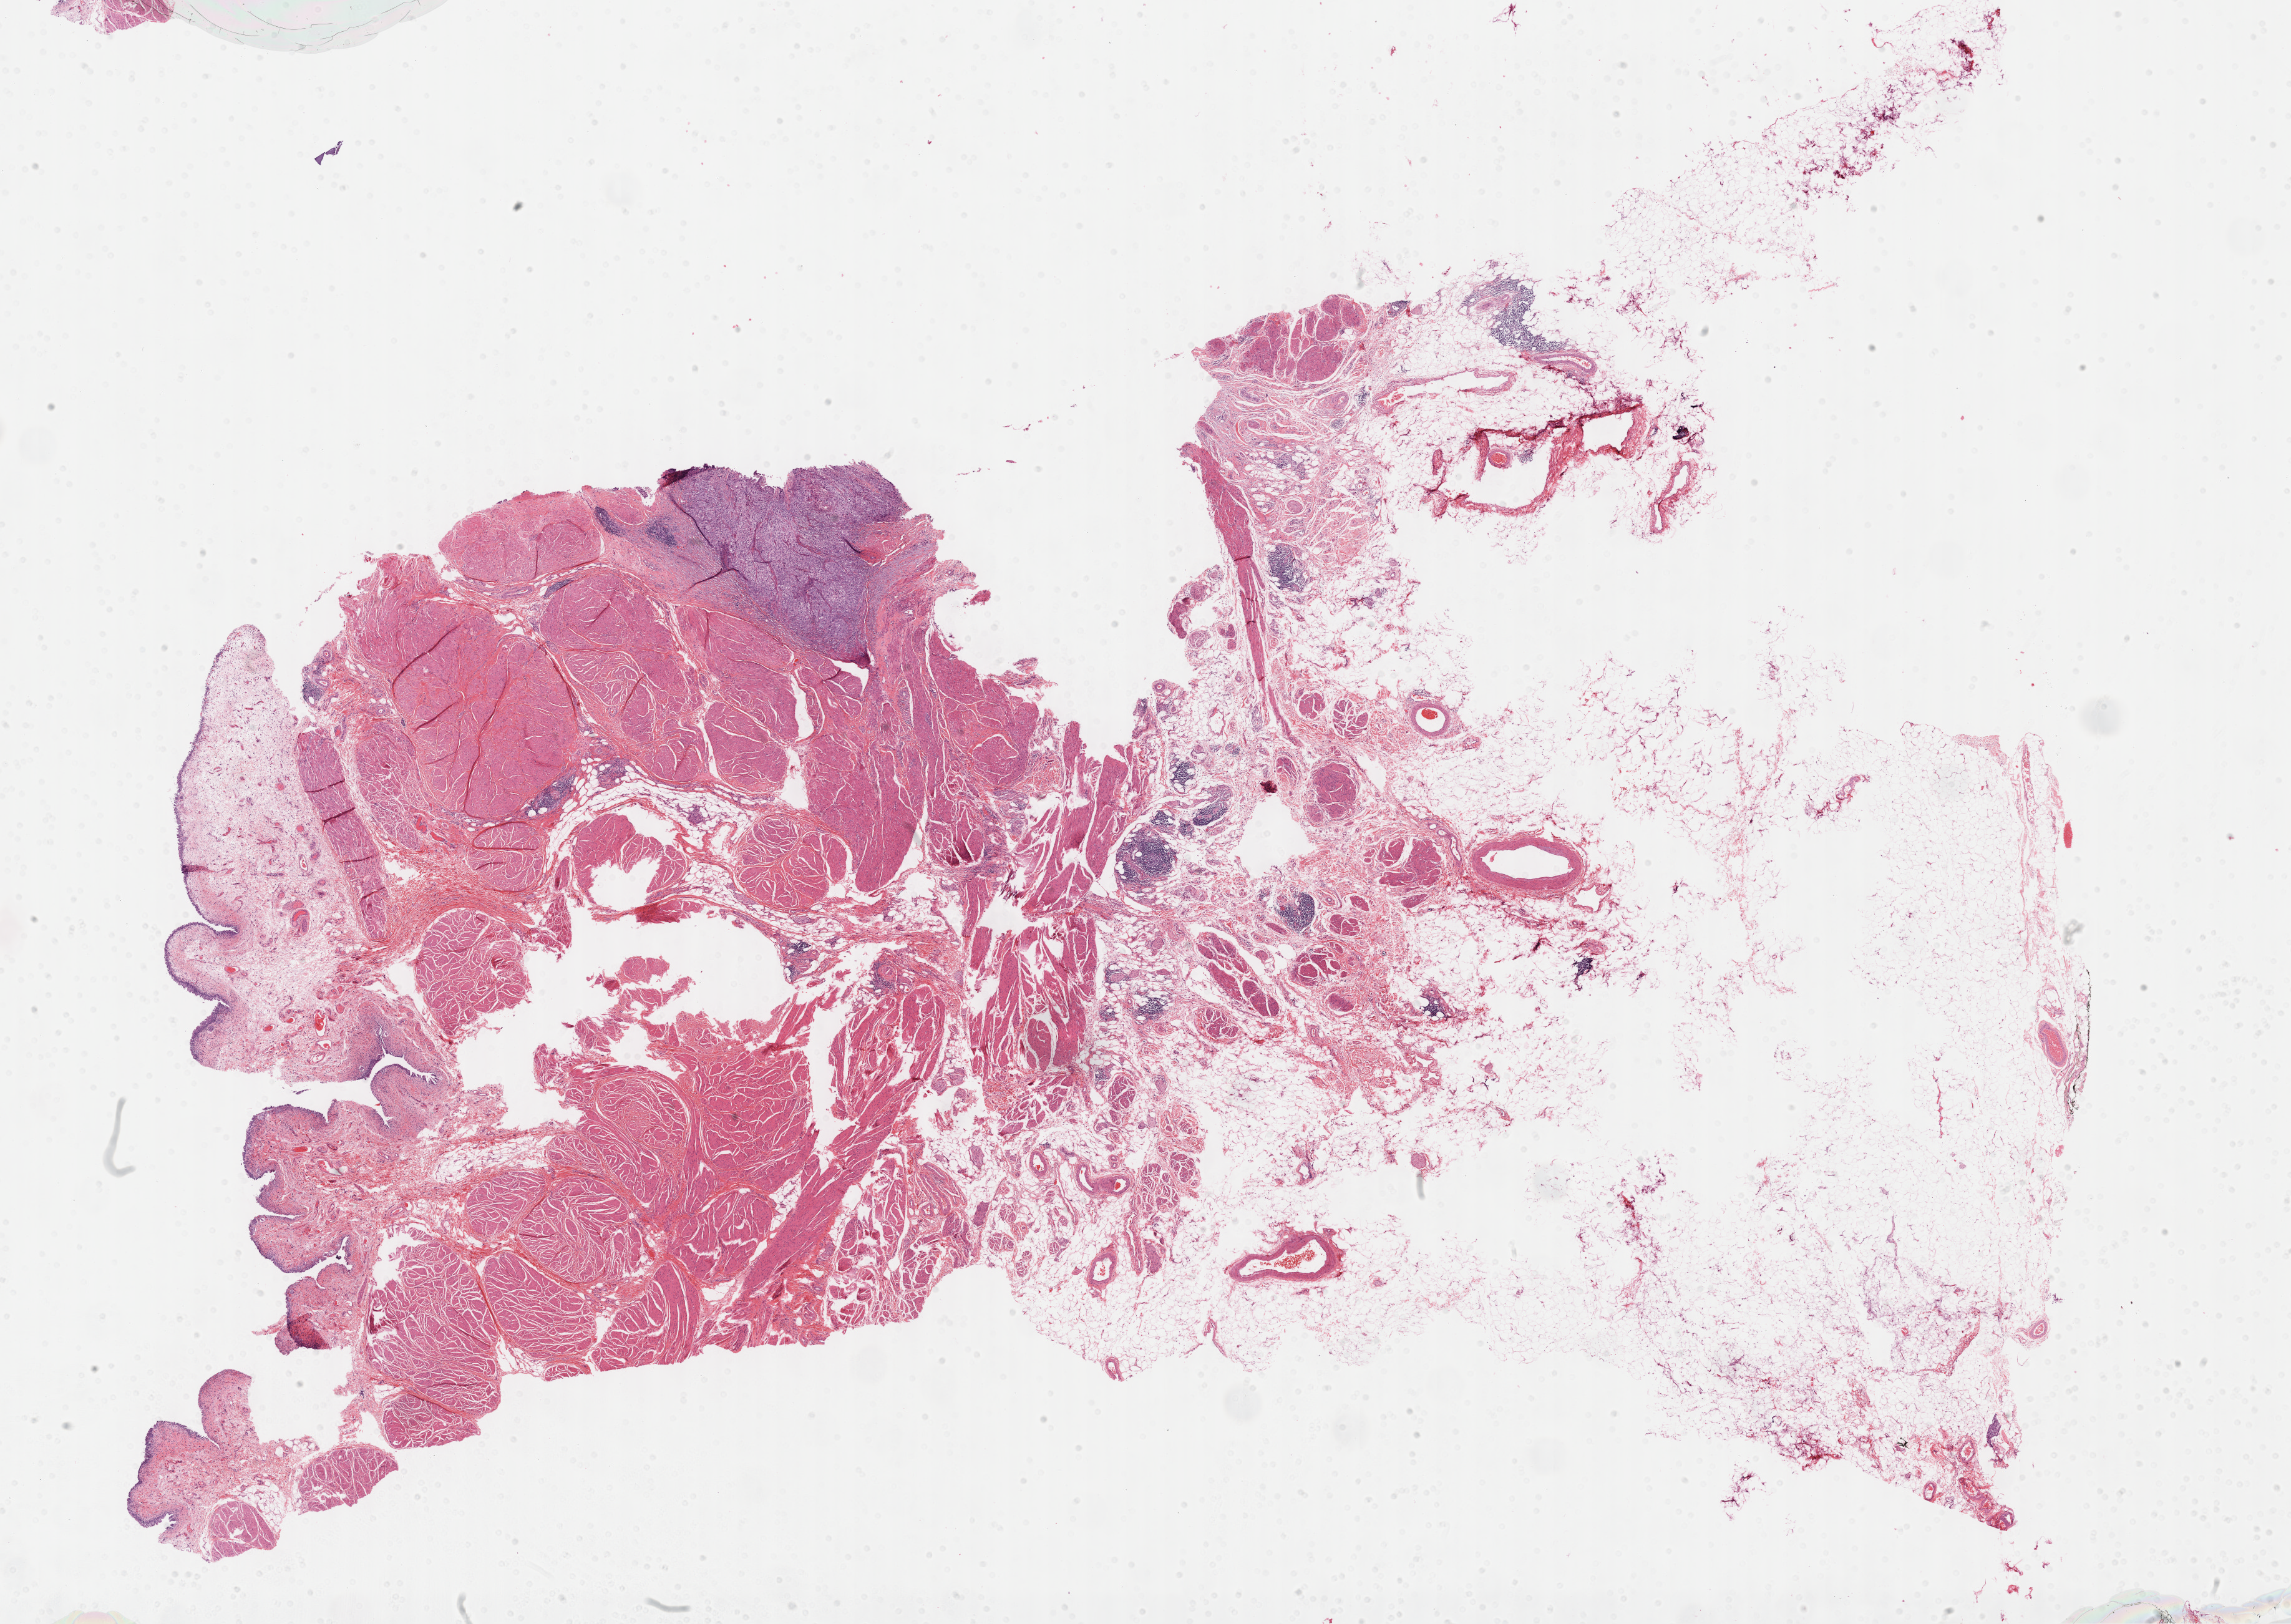
Digitized H&E-stained tissue section (whole slide), whole scanned area (about 29.7 x 21.1 mm, slide scanned at 40x) shown as a low-resolution overview. Formalin-fixed paraffin-embedded (FFPE) diagnostic section. Primary tumour sample from the bladder. Patient: male, age at initial diagnosis 62 years. Histologic grade: high grade.
• AJCC pathologic stage: IV (6th edition)
• TNM: N1 MX
• diagnosis: Papillary transitional cell carcinoma